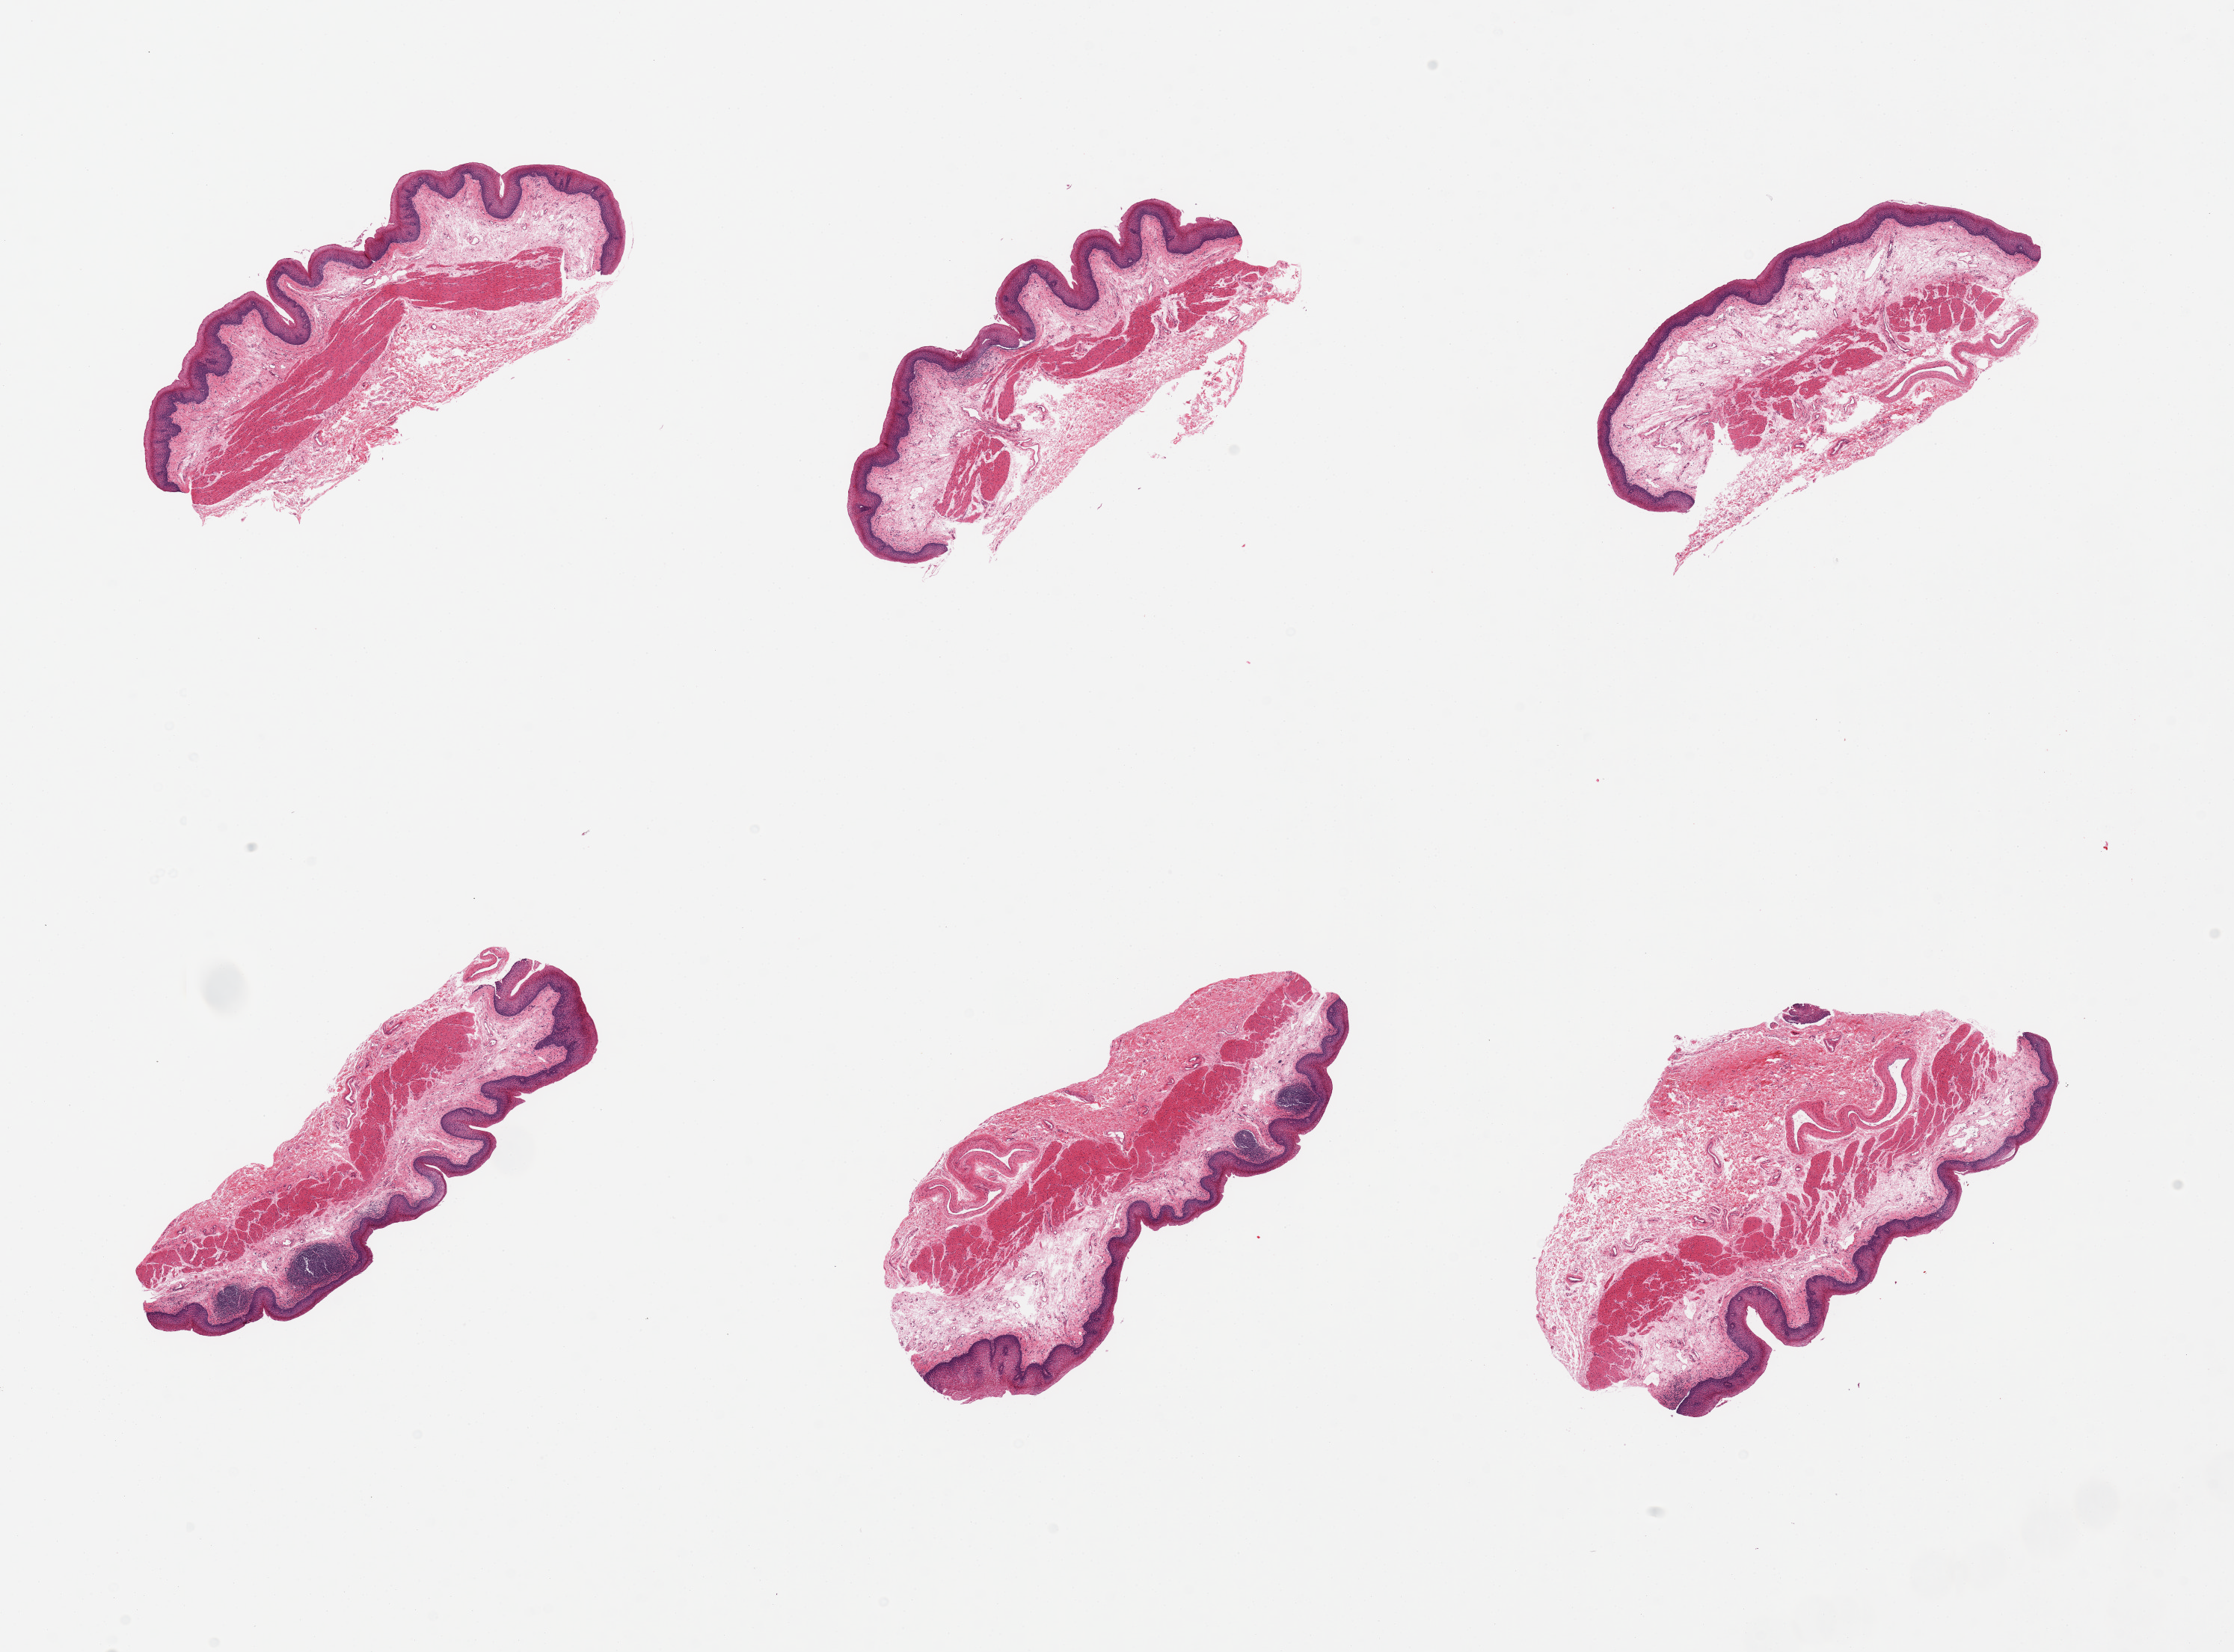
Hematoxylin and eosin (H&E) whole-slide image, a low-resolution overview of the entire scanned area, about 23.6 x 17.5 mm (from a 20x scan), PAXgene-fixed paraffin-embedded (PFPE) section, target tissue: esophageal mucous membrane, tissue donor sample. Donor: female.
Review note (as recorded): 6 pieces, squamous mucosa is ~10% thickness.